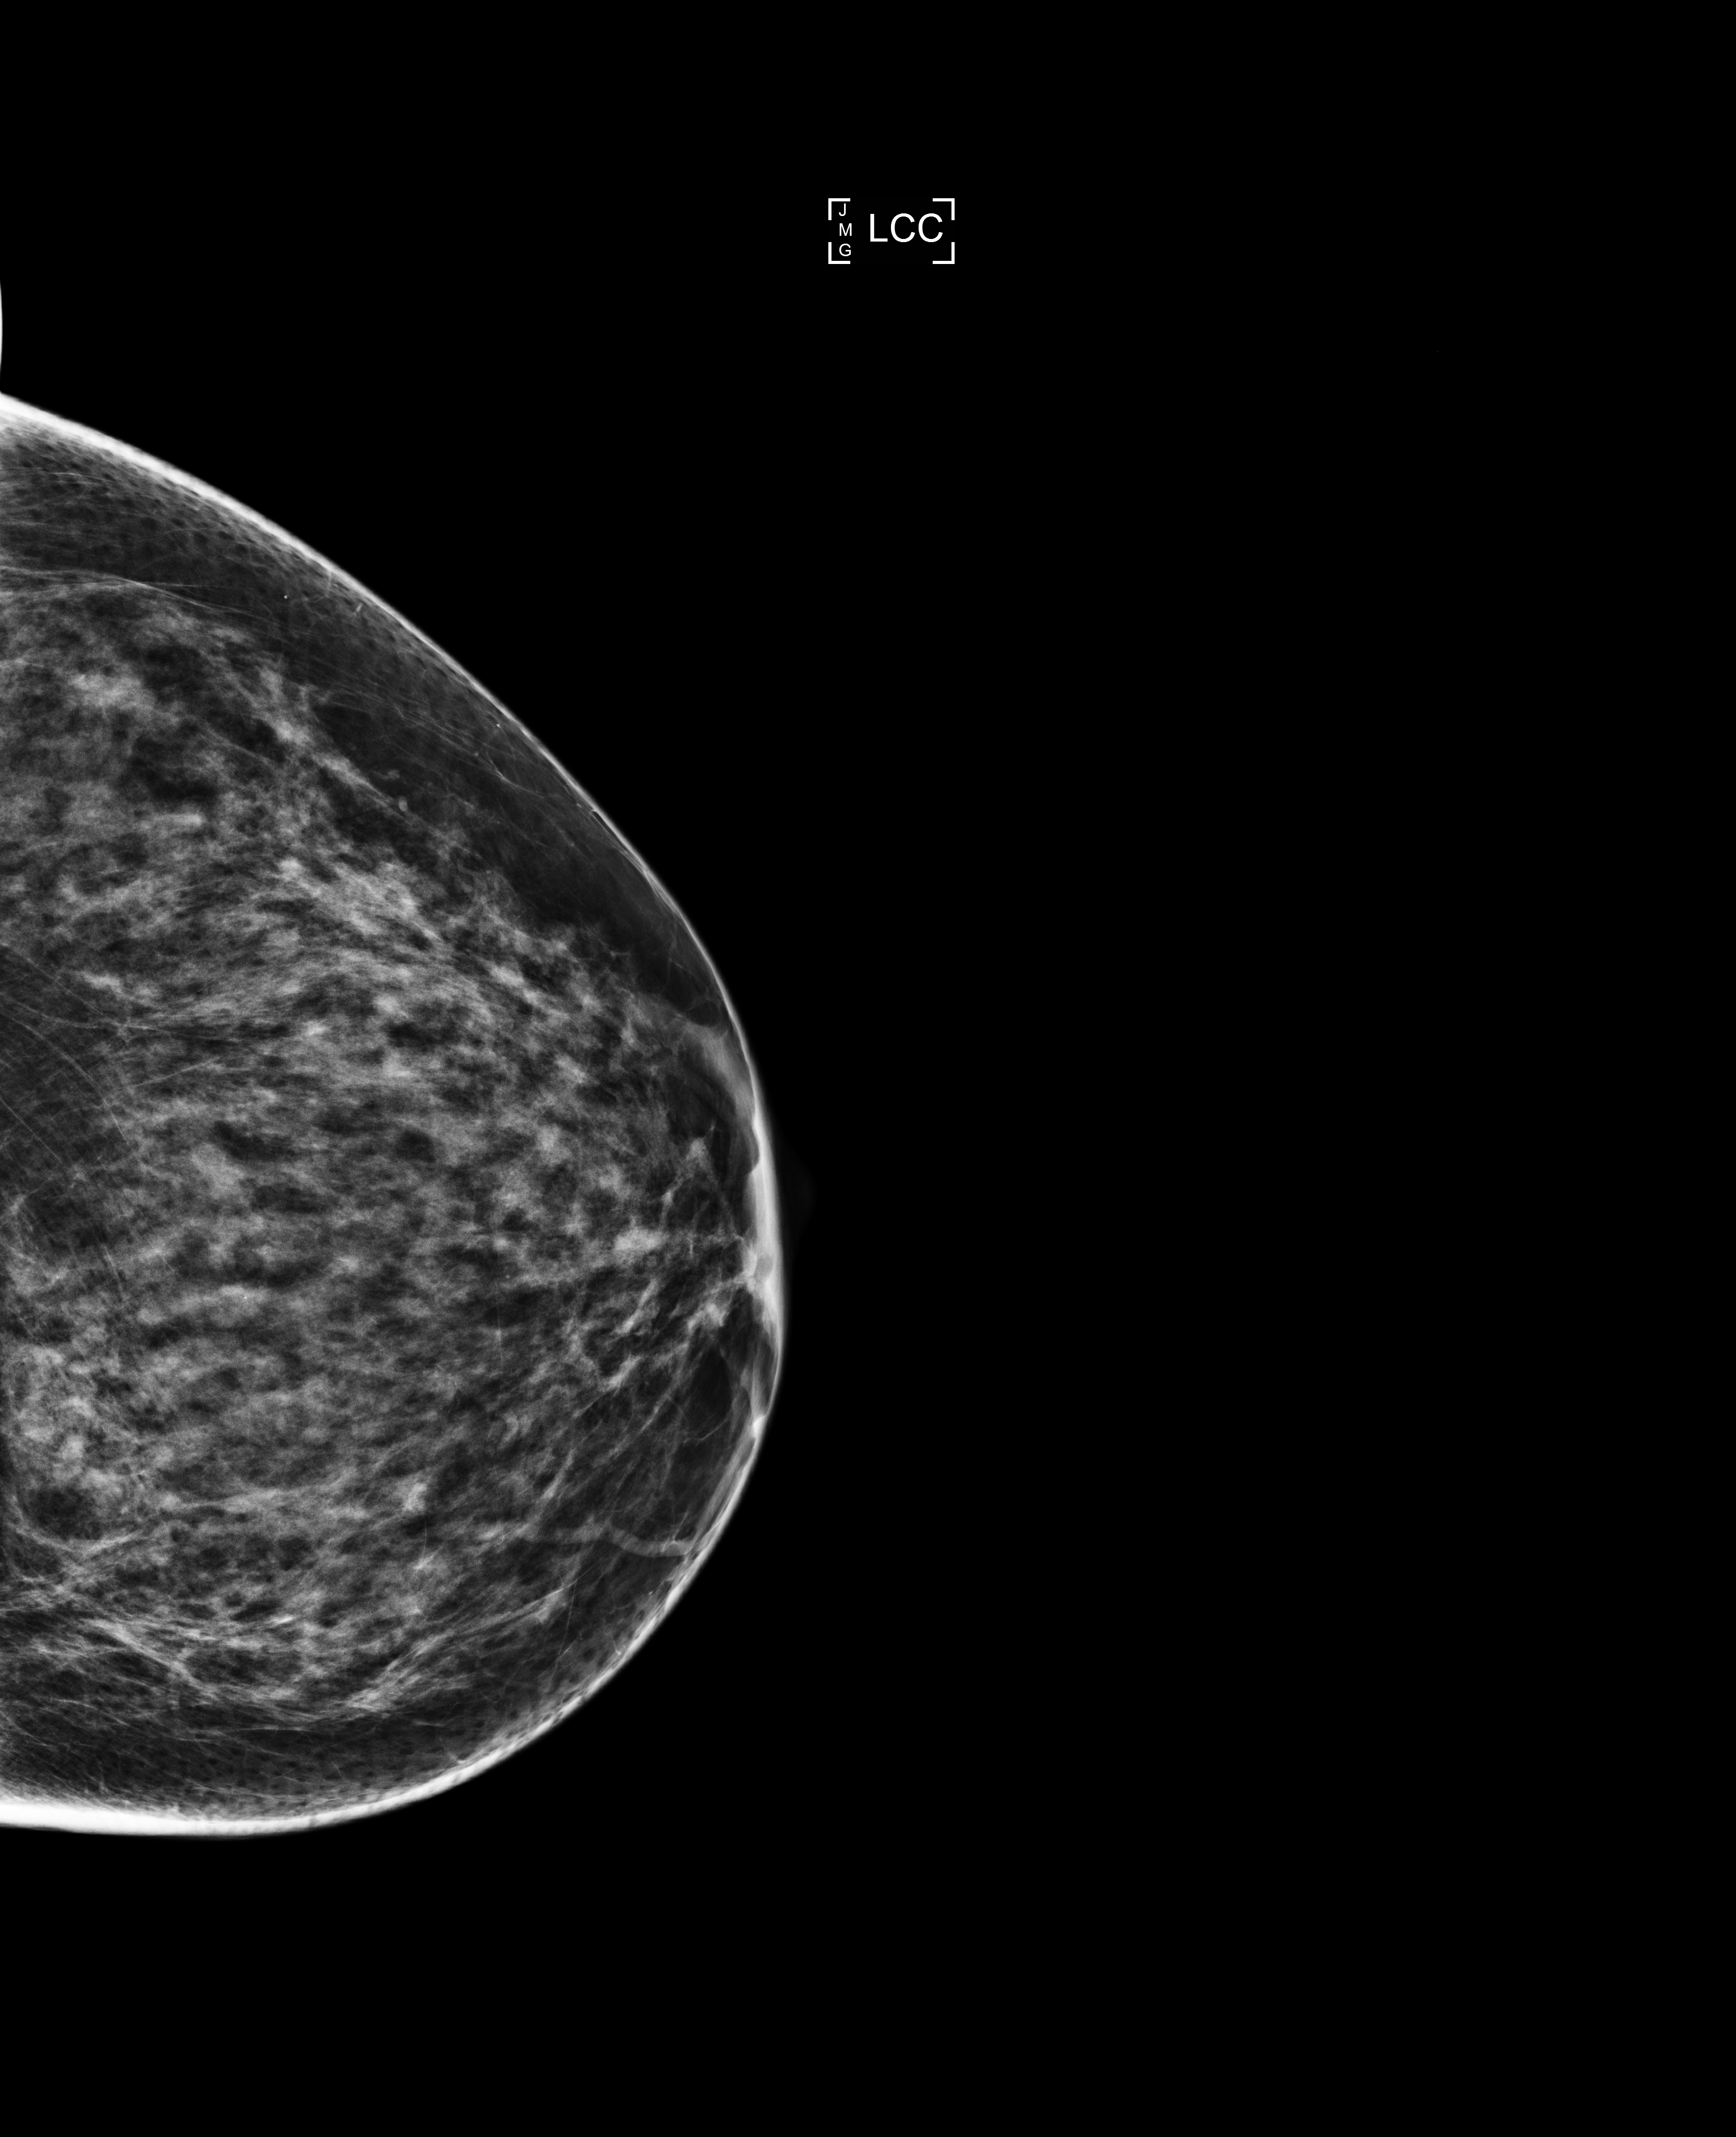
Digital mammogram (FFDM); left breast; cranio-caudal projection; screening examination. Patient: female, 55 years.
BI-RADS breast density category at the screening exam (both breasts, scale 1–4): 3. Final BI-RADS assessment for this screening round (tomosynthesis exam, both breasts): category 1. Recall: no recall after this screen.